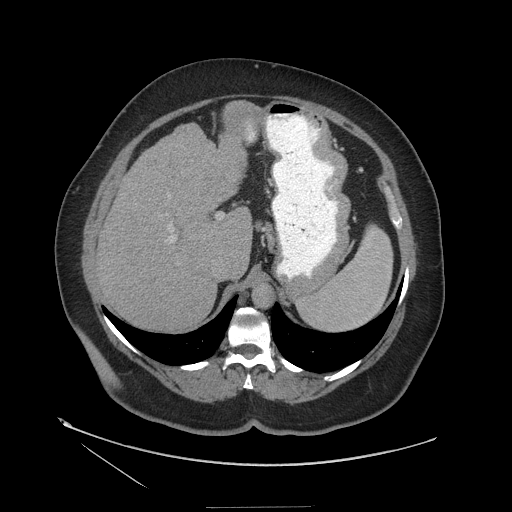
Contrast-enhanced abdominal CT (liver protocol), one axial slice. Position 82 of 127 along the scan axis. 140 kVp. Soft-tissue window (W 400 / L 40 HU). 2.5 mm slice thickness. 512 × 512 image matrix, field of view 480 × 480 mm. From the clinical record (not read from this slice): diagnosis: hepatocellular carcinoma (patient treated with transarterial chemoembolisation; whether this scan precedes or follows treatment is not stated here); TNM stage (as recorded): Stage-II; Child-Pugh class: A.
Outlined on this slice (semi-automatically segmented with operator editing):
- liver parenchyma outside the tumour (the mass and vessels are separate outlines, so this box may not span the whole liver): bounding box (x1, y1, x2, y2) in pixels: (98, 110, 258, 330)
- liver vessels: (171, 132, 255, 242)